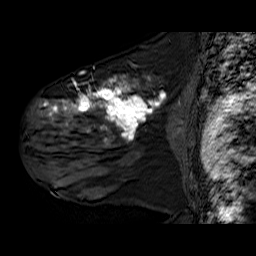
Breast MRI (dynamic contrast-enhanced), one sagittal slice; position 40 of 60 along the scan axis; dynamic contrast-enhanced series, time point 2 of 6 at this slice position (early post-contrast); 1.5 T; TE 6.3 ms, TR 32.9 ms; 4 mm slice thickness; 256 × 256 image matrix, field of view 200 × 200 mm. Female patient. From the clinical record (not read from this slice): setting: breast cancer imaged before/during neoadjuvant chemotherapy; receptor status: HER2-positive.
Structures marked on this image (semi-automatically segmented with operator editing):
- analysis volume of interest (the breast-tissue region the enhancement analysis was run in; not a lesion): bounding box <30,78,177,180> (left, top, right, bottom; pixels)
- tumour enhancement mask (voxels above the 100 % enhancement threshold inside the analysis volume of interest): <43,78,166,147>